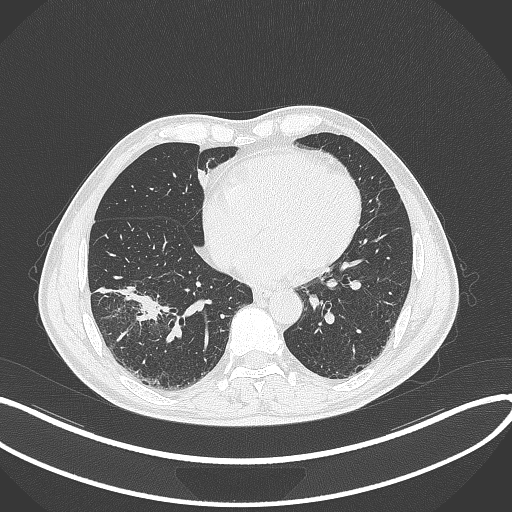
Chest CT, one axial slice; slice 129 of 364 in the series (ordered by position); lung window (W 1500 / L -600 HU); 1 mm slice thickness; 512 × 512 image matrix, field of view 400 × 400 mm. Male patient, age 58 years. Case-level facts recorded for this patient, not image findings: clinical TNM (as recorded): T3 N0 M0.
Annotated regions visible in this slice (rectangle marked by the reading radiologist):
- lung tumour (recorded histology: squamous cell carcinoma): bounding box [x1, y1, x2, y2] px = [136, 289, 167, 321]